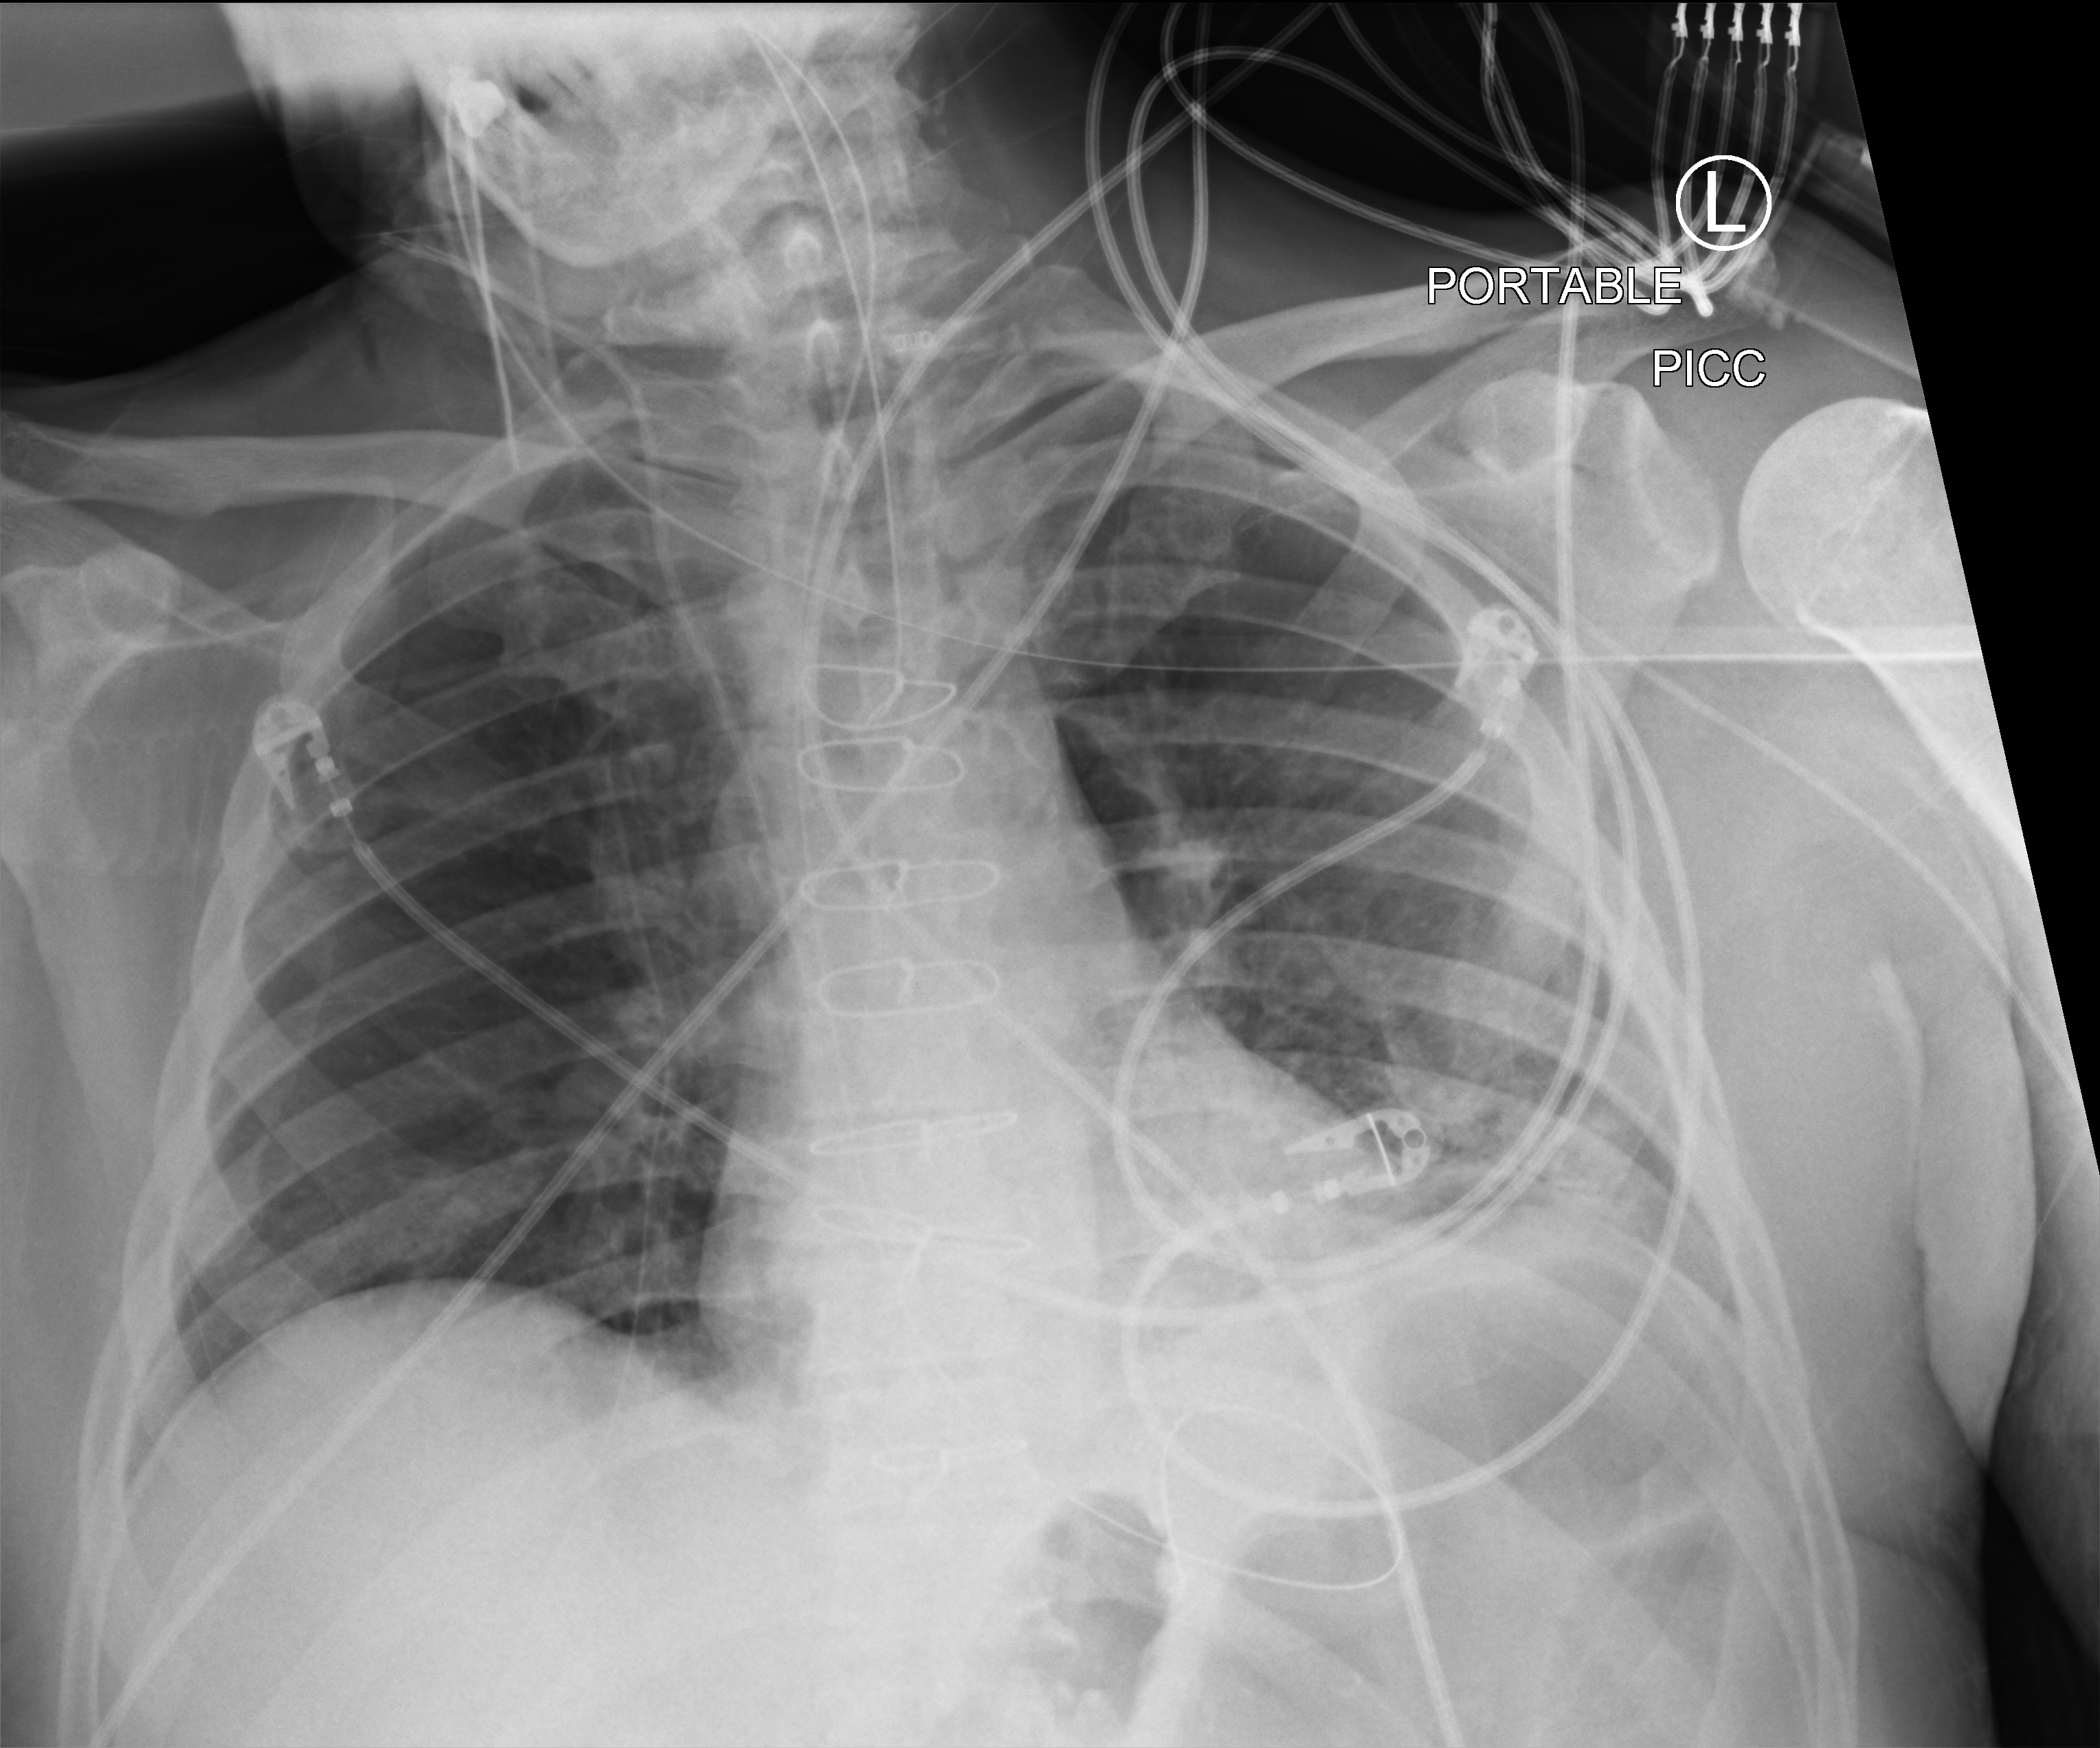
Chest X-ray (portable); anteroposterior (AP) projection. Male patient hospitalised with COVID-19, age 60–74 years.
Hospital-stay facts (about this admission, not read from this image; timing relative to this image not recorded):
- mechanically ventilated during this hospital stay: yes
- admitted to intensive care during this hospital stay: yes
- length of hospital stay: 44 days